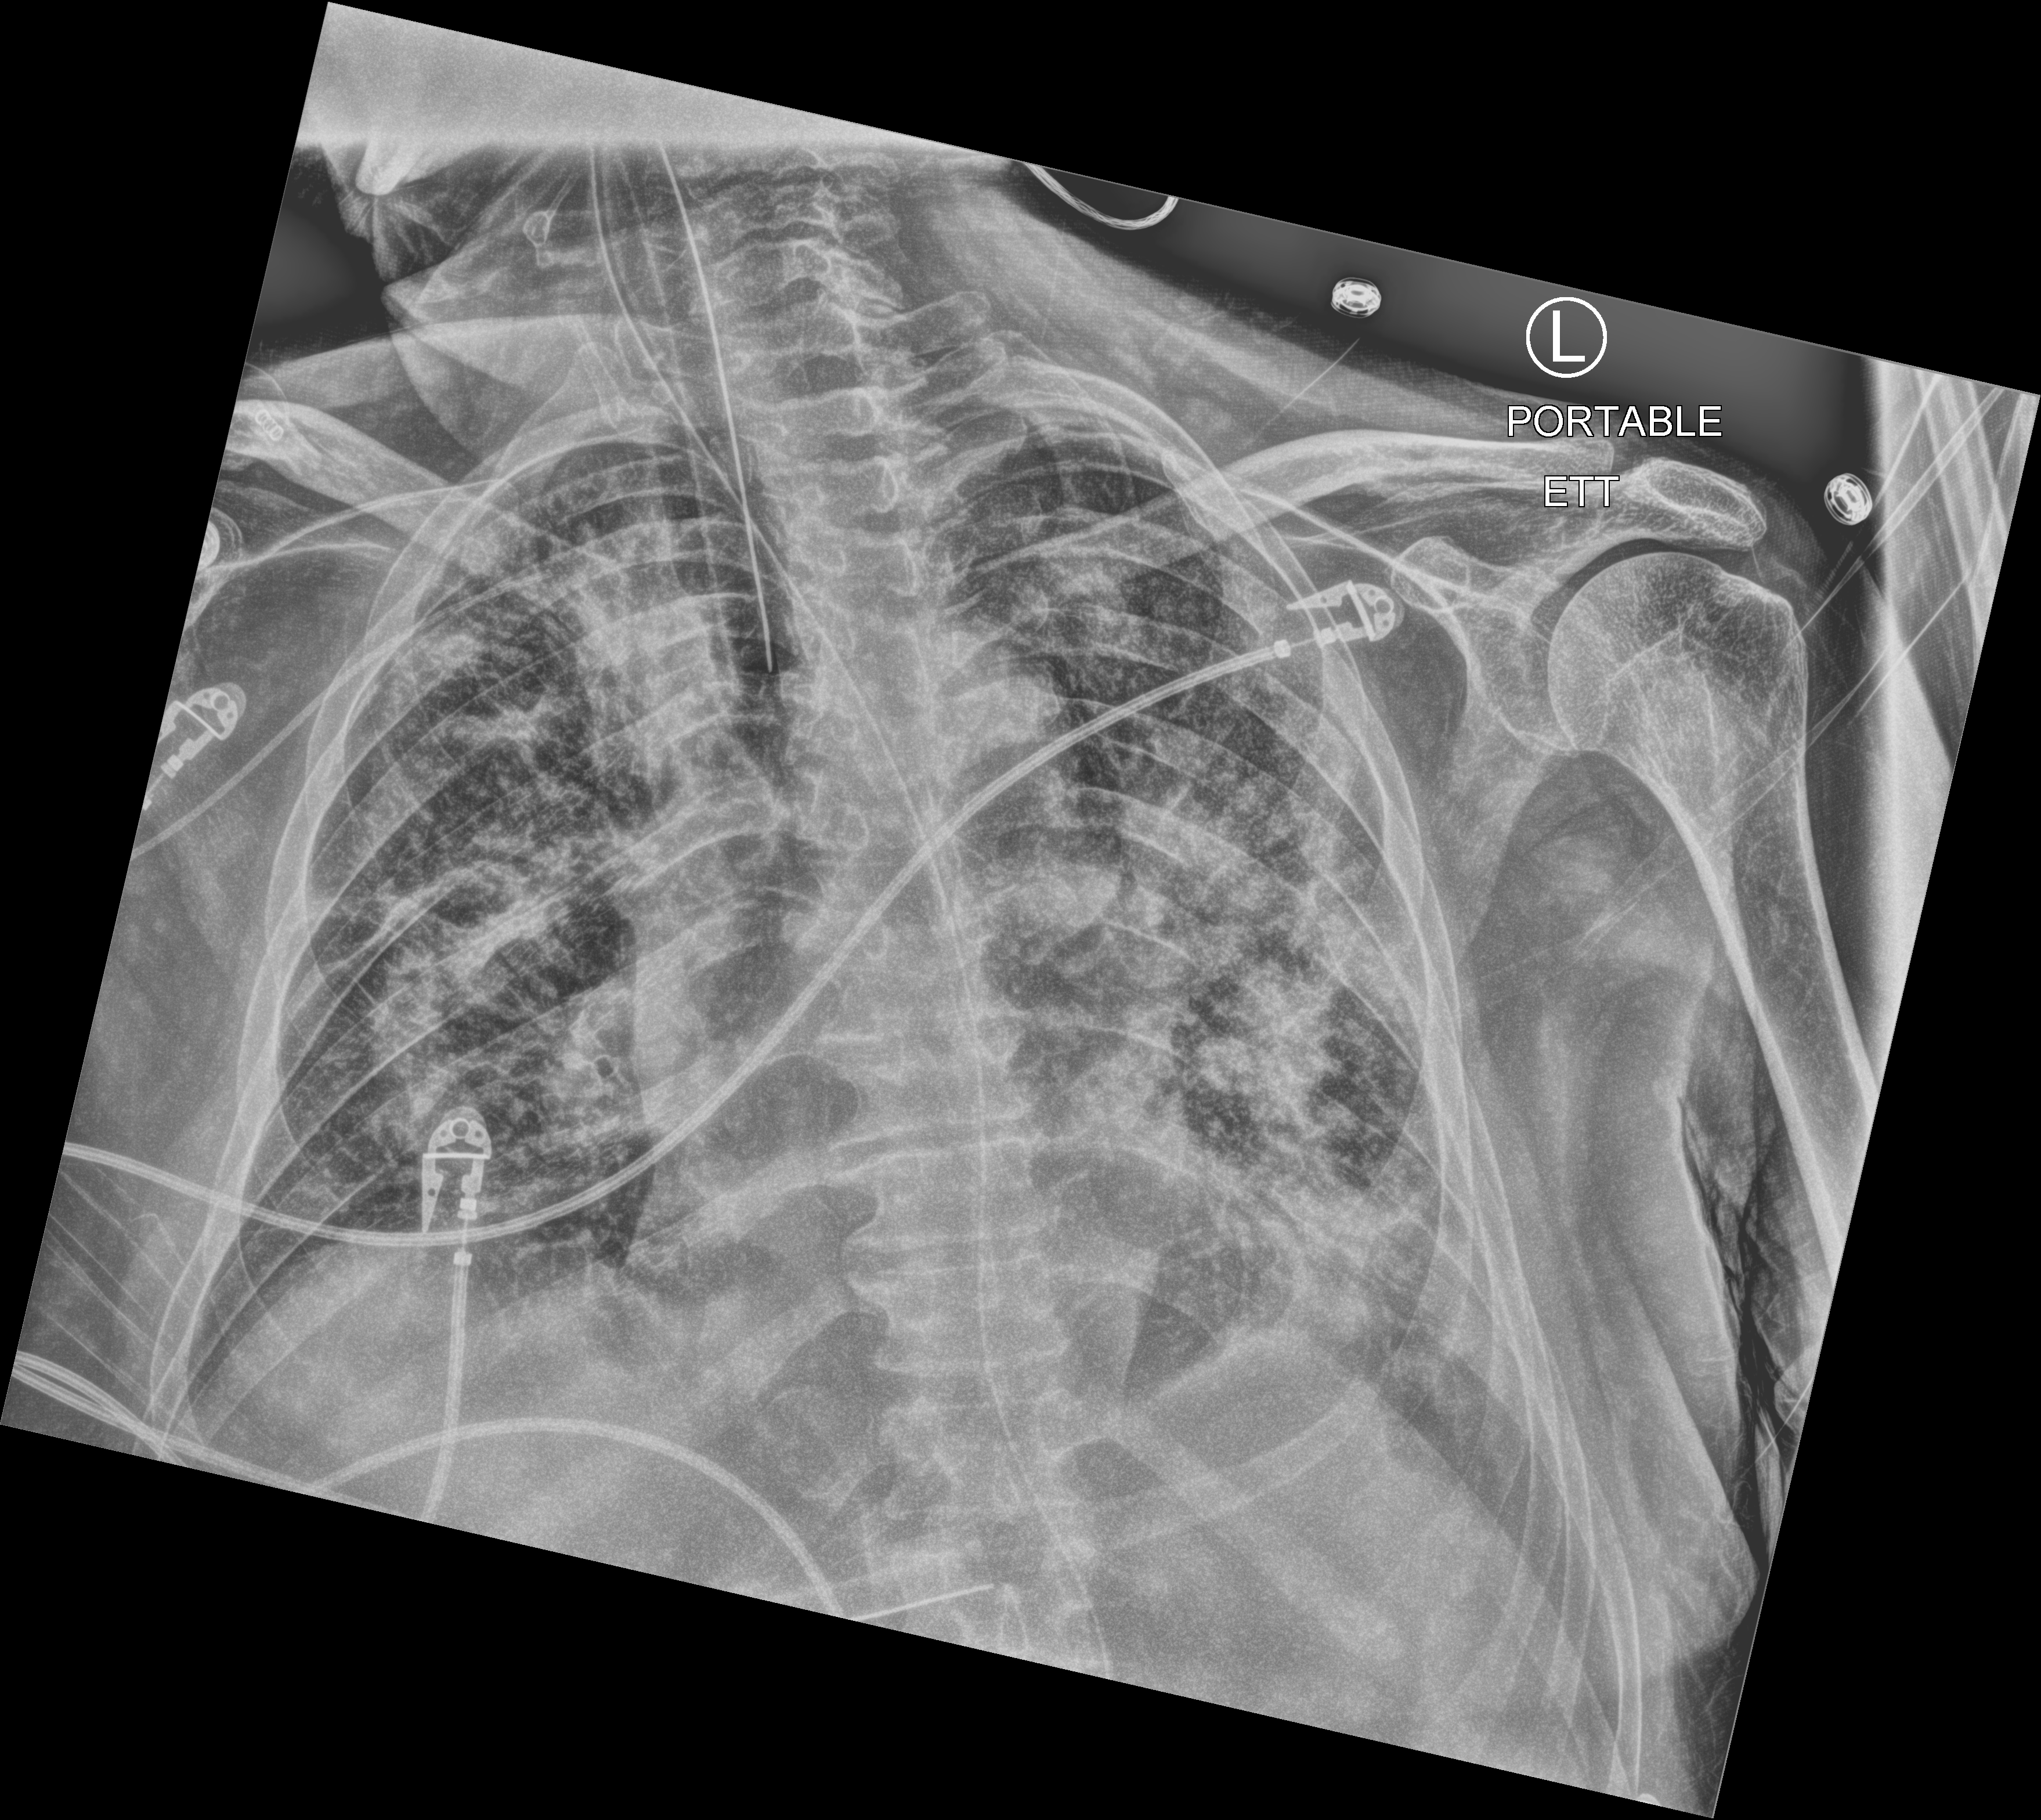
Bedside chest radiograph (computed radiography); anteroposterior (AP) projection. Male patient hospitalised with COVID-19, age 60–74 years.
From the hospital-stay record, not from the radiograph (when in the stay this image was taken is not recorded): length of hospital stay: 24 days; mechanically ventilated during this hospital stay: yes; admitted to intensive care during this hospital stay: yes.